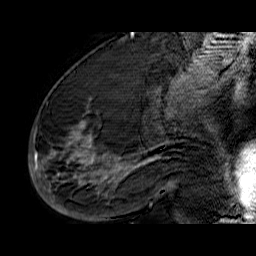
Breast MRI (dynamic contrast-enhanced), one sagittal slice; position 33 of 60 along the scan axis; dynamic contrast-enhanced series, time point 2 of 6 at this slice position (early post-contrast); 1.5 T; TE 6.5 ms, TR 32.9 ms; 256 × 256 image matrix, field of view 200 × 200 mm. Female patient. Case-level facts recorded for this patient, not image findings: setting: breast cancer imaged before/during neoadjuvant chemotherapy; receptor status: HR-positive, HER2-negative.
Structures marked on this image (semi-automatically segmented with operator editing):
- analysis volume of interest (the breast-tissue region the enhancement analysis was run in; not a lesion): bounding box <33,74,176,210> (left, top, right, bottom; pixels)
- tumour enhancement mask (voxels above the 100 % enhancement threshold inside the analysis volume of interest): <33,100,171,190>